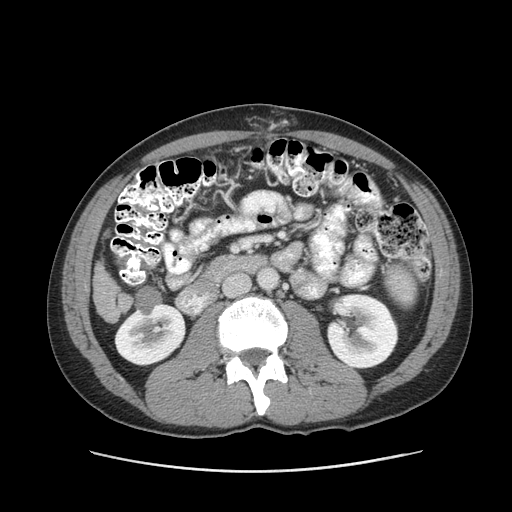
Contrast-enhanced abdominal CT (liver protocol), one axial slice; 120 kVp; soft-tissue window (W 400 / L 40 HU); 2.5 mm slice thickness; 512 × 512 image matrix, field of view 380 × 380 mm. From the clinical record (not read from this slice): diagnosis: hepatocellular carcinoma (patient treated with transarterial chemoembolisation; whether this scan precedes or follows treatment is not stated here); TNM stage (as recorded): Stage-II; Child-Pugh class: A; tumour differentiation: moderately differentiated; tumour size: 1 cm.
Outlined on this slice (semi-automatically segmented with operator editing):
- liver parenchyma outside the tumour (the mass and vessels are separate outlines, so this box may not span the whole liver): bounding box <94,262,120,320> (left, top, right, bottom; pixels)